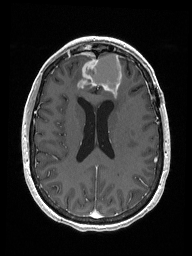
Brain MRI from a brain-tumour surgery series, one axial slice. Position 70 of 192 along the scan axis. T1-weighted post-contrast. 1 mm slice thickness. 192 × 256 image matrix, field of view 187 × 250 mm. Case-level facts recorded for this patient, not image findings: histopathology: Metastastic Carcinoma from Breast primary; tumour location: Right Frontal.
Structures marked on this image (expert manual segmentation):
- previous resection cavity: bounding box (x1, y1, x2, y2) in pixels: (86, 52, 122, 95)